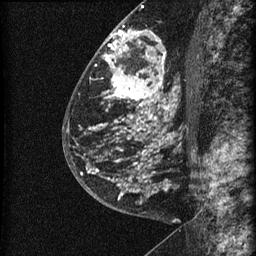
Breast MRI (dynamic contrast-enhanced), one sagittal slice. Slice 32 of 60 in the series (ordered by position). Dynamic contrast-enhanced series, image 2 of 3 at this slice position (ordered by acquisition). 1.5 T. TE 4.2 ms, TR 22.7 ms. 1.5 mm slice thickness. 256 × 256 image matrix, field of view 180 × 180 mm. Patient: female, 48 years. From the clinical record (not read from this slice): setting: breast cancer imaged before/during neoadjuvant chemotherapy; receptor status: triple-negative.
Outlined on this slice (semi-automatically segmented with operator editing):
- analysis volume of interest (the breast-tissue region the enhancement analysis was run in; not a lesion): bounding box <81,23,186,202> (left, top, right, bottom; pixels)
- tumour enhancement mask (voxels above the 90 % enhancement threshold inside the analysis volume of interest): <81,30,168,198>